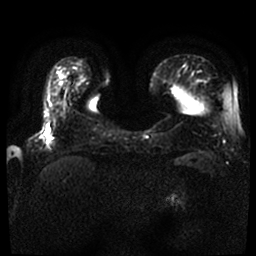
Breast MRI, one axial slice; position 11 of 59 along the scan axis; diffusion-weighted series; image 2 of 4 stored at this slice position (different b-values; order by instance number); 1.5 T; 4 mm slice thickness; 256 × 256 image matrix, field of view 360 × 360 mm. Female patient.
Outlined on this slice (outlined manually by an expert reader):
- tumour on diffusion-weighted imaging: bounding box [x1, y1, x2, y2] px = [45, 127, 51, 139]